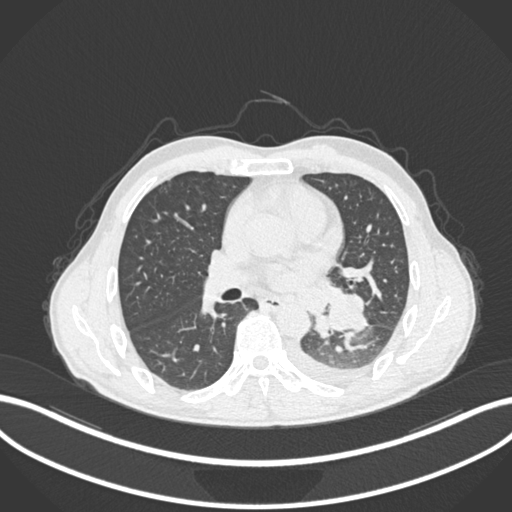
Chest CT, one axial slice; position 128 of 222 along the scan axis; reconstruction kernel B30f; 120 kVp; lung window (W 1500 / L -600 HU); 1 mm slice thickness; 512 × 512 image matrix, field of view 400 × 400 mm. Male patient, age 47 years. Case-level facts recorded for this patient, not image findings: clinical TNM (as recorded): T3 N1 M1c; histopathological grade: G3.
Structures marked on this image (bounding box drawn by a radiologist):
- lung tumour (recorded histology: small cell carcinoma): box from (x=308, y=288) to (x=368, y=343) px